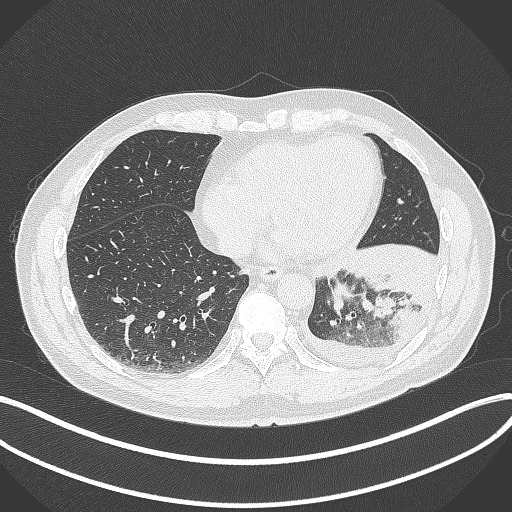
Chest CT, one axial slice. Slice 109 of 342 in the series (ordered by position). 120 kVp. Lung window (W 1500 / L -600 HU). 1 mm slice thickness. 512 × 512 image matrix, field of view 400 × 400 mm. Patient: male, 58 years. Case-level facts recorded for this patient, not image findings: clinical TNM (as recorded): T3 N1 M1b.
Annotated regions visible in this slice (rectangle marked by the reading radiologist):
- lung tumour (recorded histology: small cell carcinoma): bounding box [x1, y1, x2, y2] px = [325, 271, 355, 325]